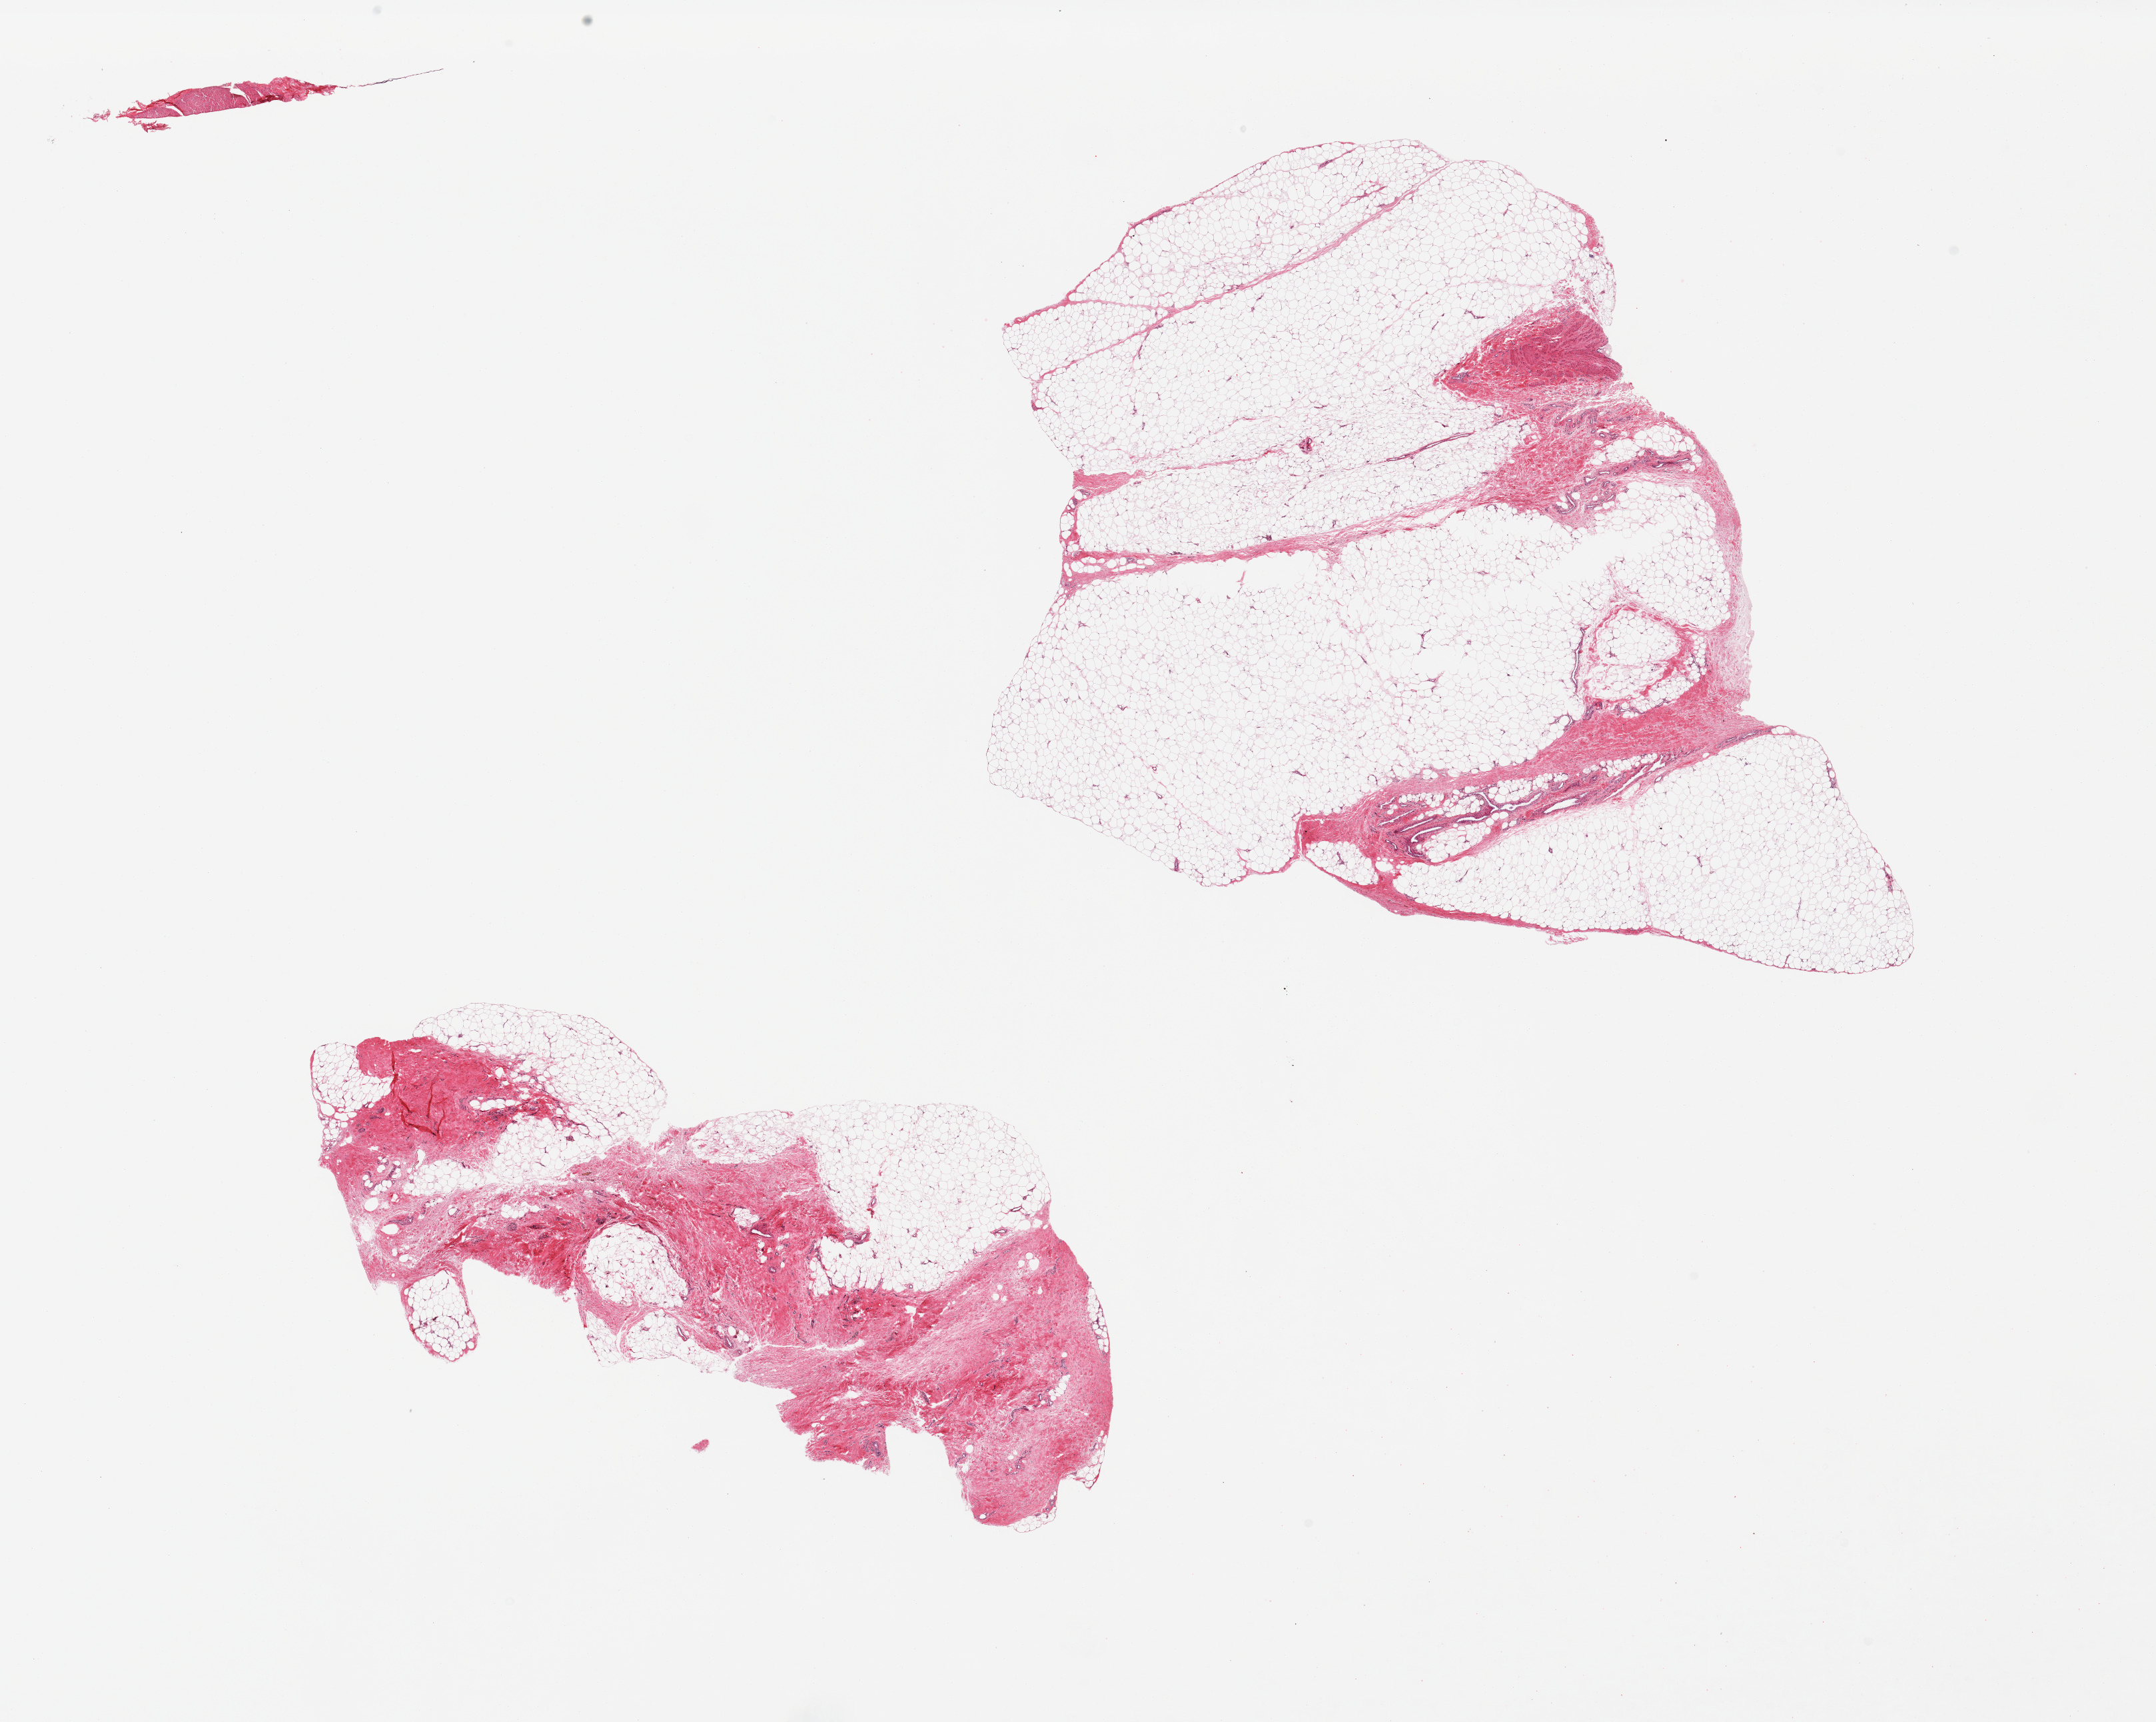
Haematoxylin and eosin whole-slide image, brightfield, whole scanned area (about 25.6 x 20.4 mm, from a 20x scan) shown as a low-resolution overview, PAXgene-fixed, paraffin-embedded tissue, target tissue: adipose tissue, tissue donor sample. Donor: male.
Review note (as recorded): 2 pieces, ~50% fibrovascular elements.